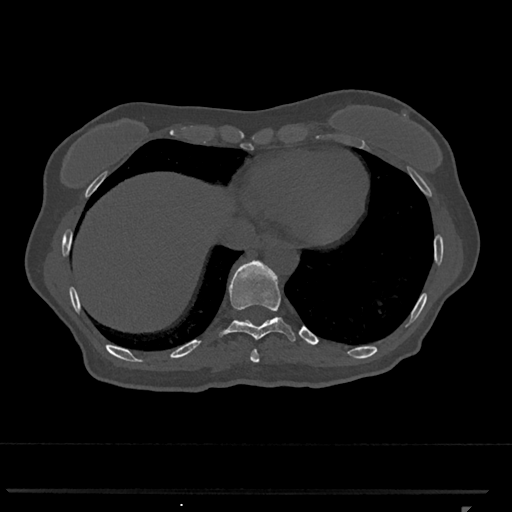
CT including the spine, one axial slice; position 569 of 793 along the scan axis; reconstruction kernel Br40s/3; 120 kVp; bone window (W 1800 / L 400 HU); 0.5 mm slice thickness; 512 × 512 image matrix. Patient: female, 62 years. From the clinical record (not read from this slice): primary cancer: renal.
Annotated regions visible in this slice (semi-automatically segmented with operator editing):
- T10 vertebra: bounding box [x1, y1, x2, y2] px = [219, 260, 296, 342]
- T9 vertebra: [250, 349, 260, 363]